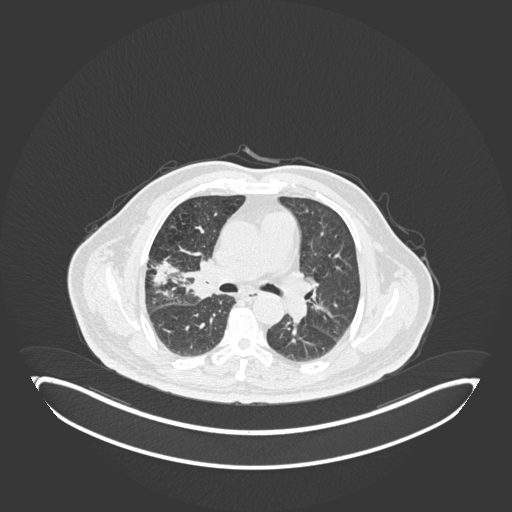
Chest CT, one axial slice. Position 101 of 247 along the scan axis. Reconstruction kernel B30f. Lung window (W 1500 / L -600 HU). 512 × 512 image matrix. Patient: male, 72 years. From the clinical record (not read from this slice): clinical TNM (as recorded): T1c N0 M0.
Structures marked on this image (rectangle marked by the reading radiologist):
- lung tumour (recorded histology: squamous cell carcinoma): box from (x=182, y=253) to (x=213, y=307) px